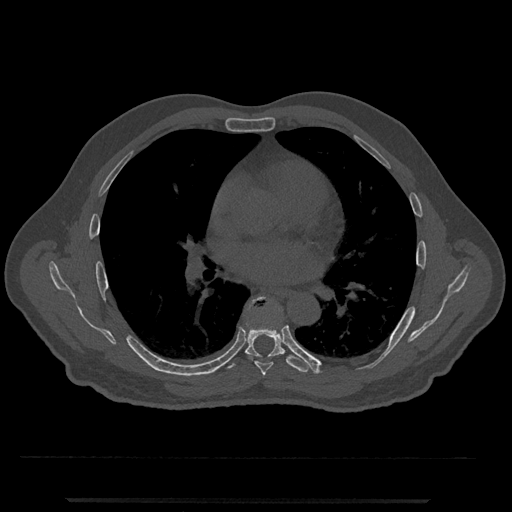
CT including the spine, one axial slice. Slice 710 of 797 in the series (ordered by position). Reconstruction kernel Br40s/3. 120 kVp. Bone window (W 1800 / L 400 HU). 0.5 mm slice thickness. 512 × 512 image matrix, field of view 419 × 419 mm. Patient: male, 63 years. Case-level facts recorded for this patient, not image findings: primary cancer: prostate.
Structures marked on this image (semi-automatically segmented with operator editing):
- T6 vertebra: bounding box <245,297,273,376> (left, top, right, bottom; pixels)
- T7 vertebra: <221,300,320,374>